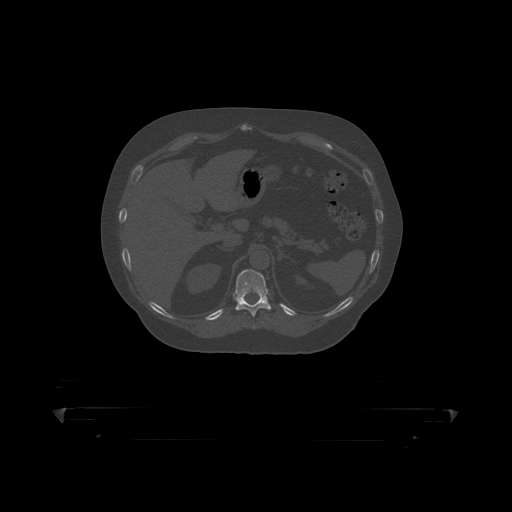
CT including the spine, one axial slice. Position 195 of 390 along the scan axis. Reconstruction kernel STANDARD. 120 kVp. Bone window (W 1800 / L 400 HU). 1.25 mm slice thickness. 512 × 512 image matrix, field of view 650 × 650 mm. Male patient, age 60 years. From the clinical record (not read from this slice): primary cancer: prostate.
Structures marked on this image (semi-automatically segmented with operator editing):
- T11 vertebra: bounding box [x1, y1, x2, y2] px = [223, 270, 290, 317]